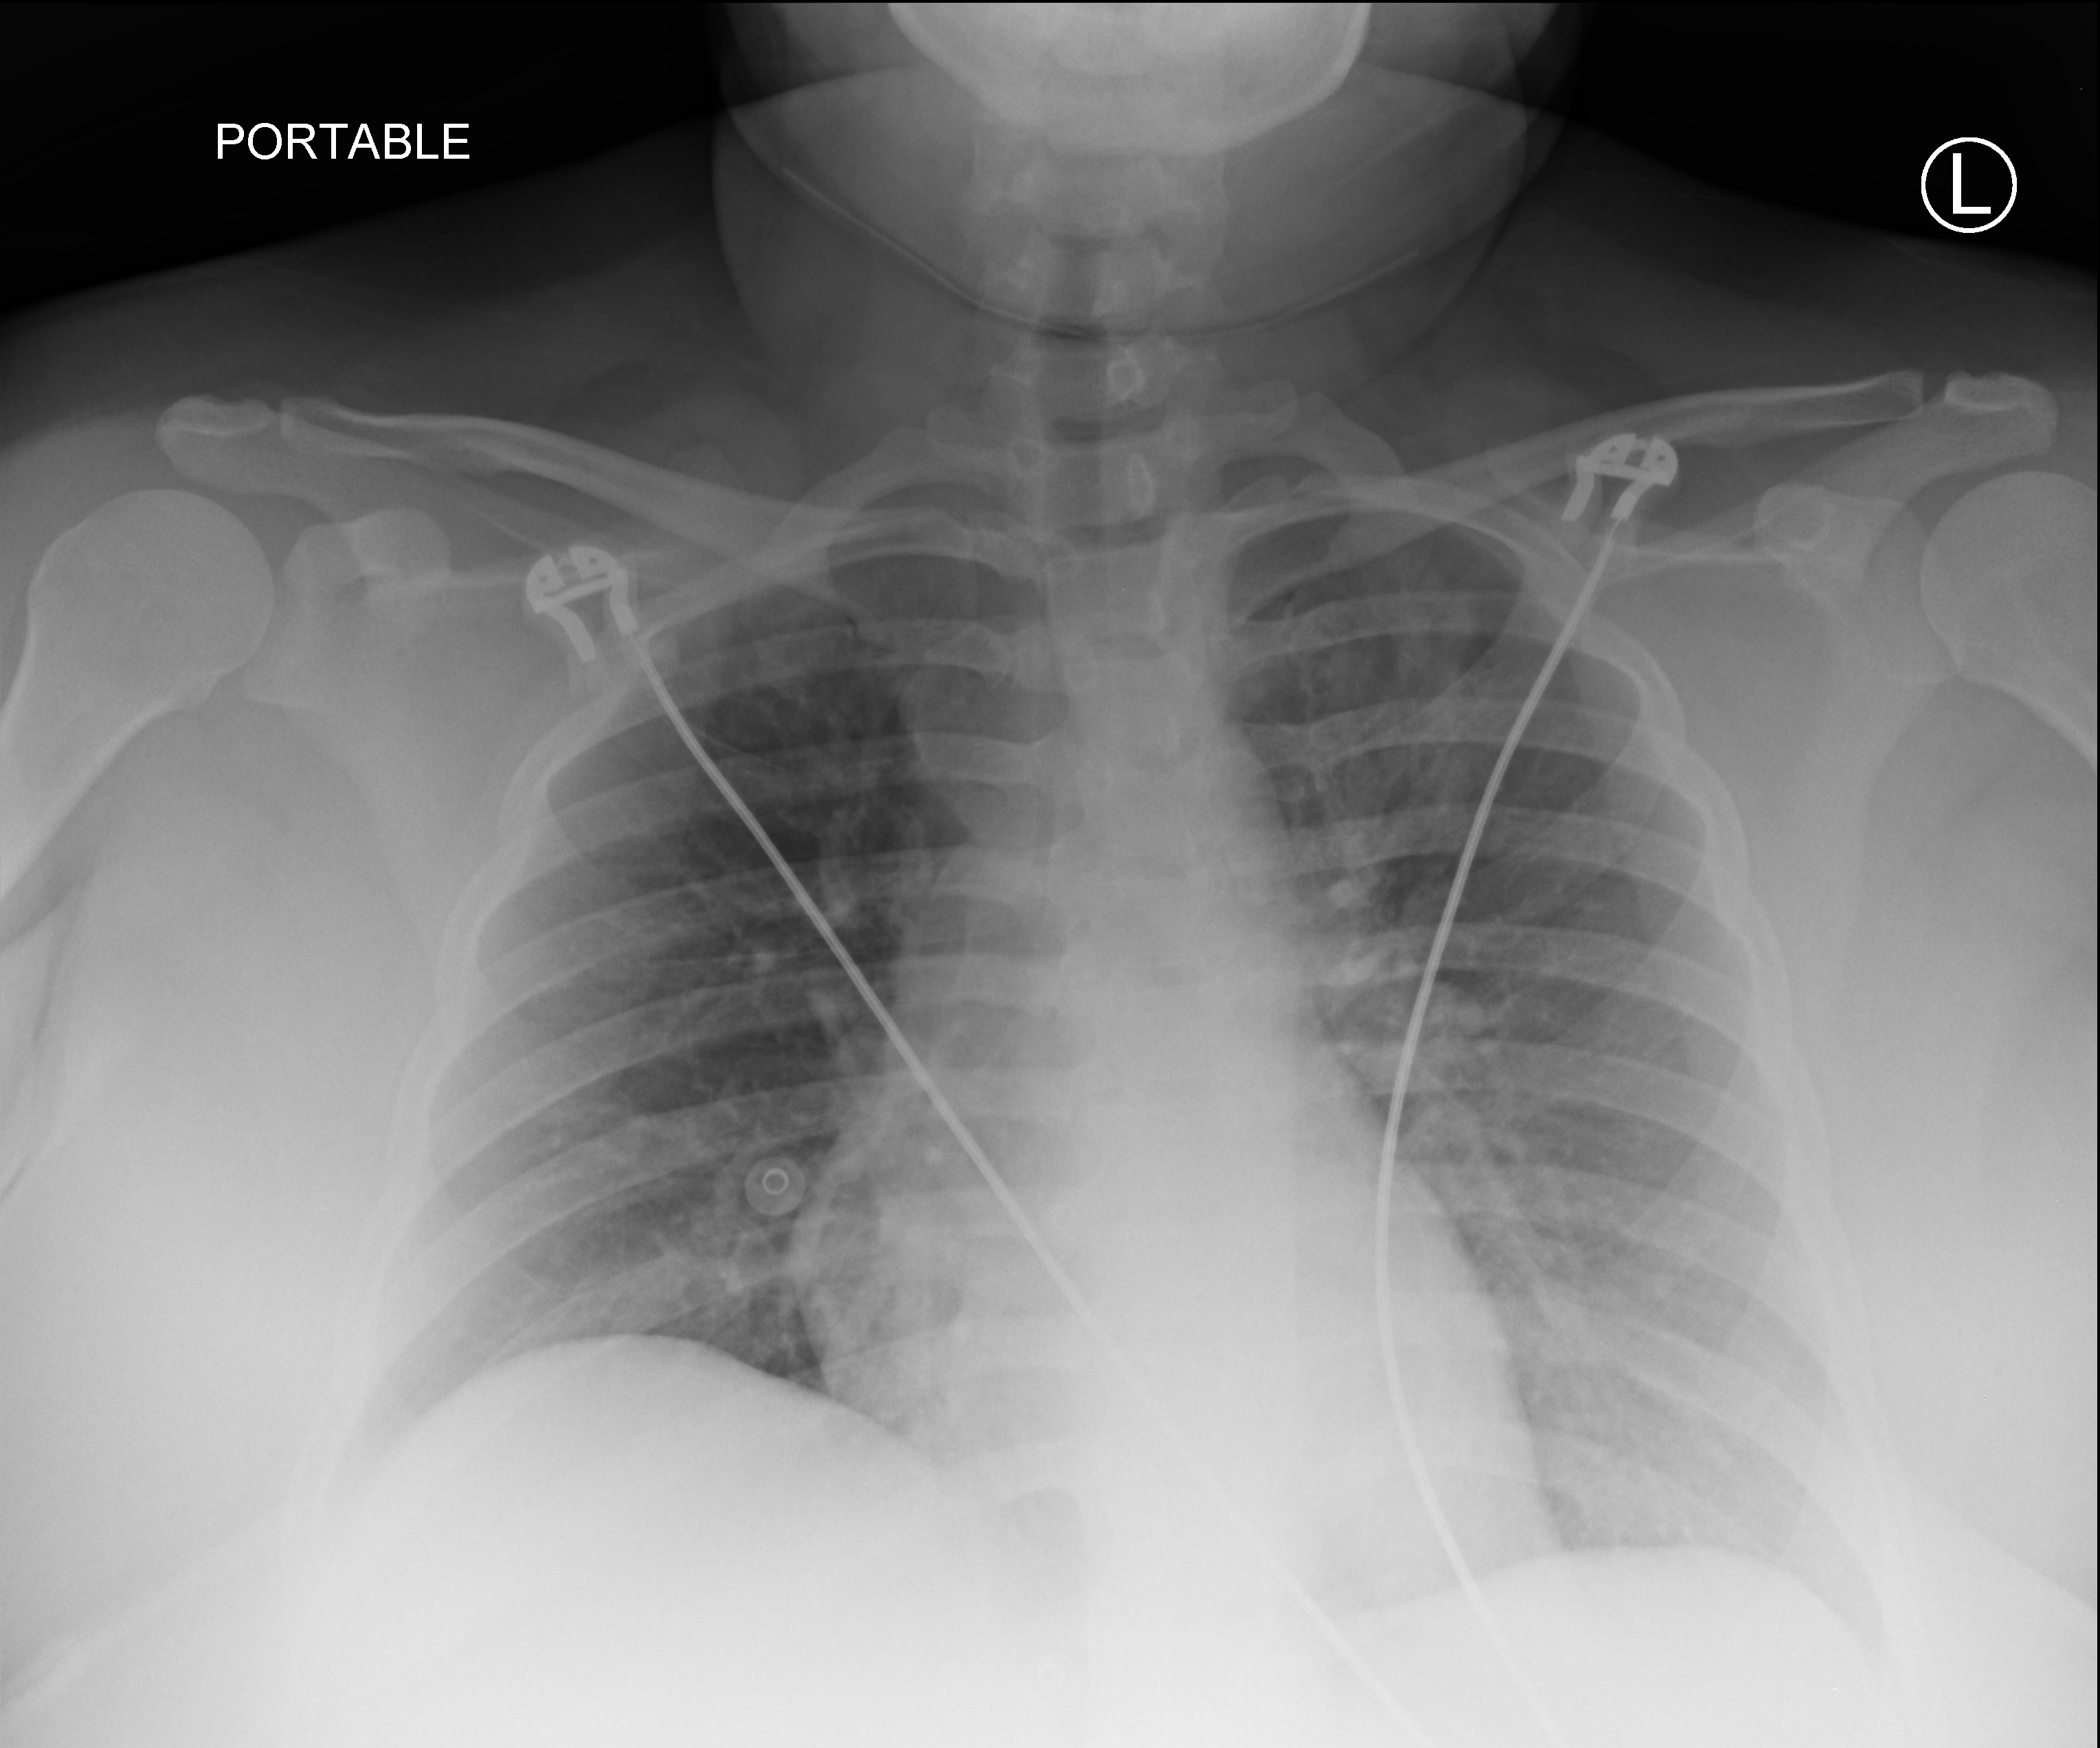
Portable chest radiograph, anteroposterior (AP) projection. Patient hospitalised with COVID-19; female, aged 18–59 years.
Admission-level facts for this patient (not findings on this image; timing relative to this image not recorded): chronic kidney disease (admission record): no; mechanically ventilated during this hospital stay: no.